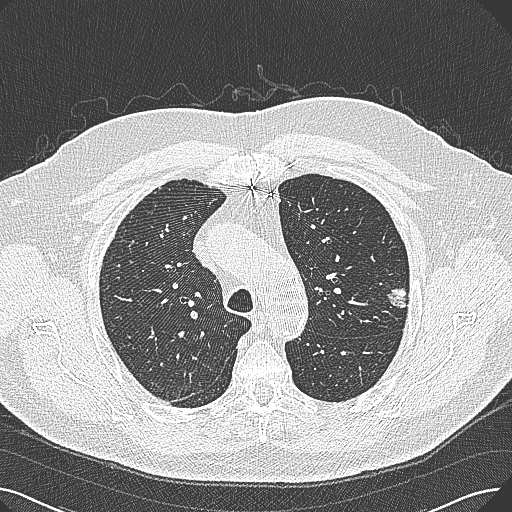
Axial slice from a low-dose chest CT screening exam, baseline screening round, lung window (W 1500 / L -600 HU), lung (sharp) reconstruction kernel (B80f). Male participant, aged 74 years at enrolment. Former smoker at enrolment.
Lesion marked by an expert reader, bounding box <376,273,423,317> (left, top, right, bottom; pixels). Screening reader's record for this exam (one nodule recorded; not confirmed to be the boxed lesion): non-calcified nodule or mass ≥4 mm, left upper lobe, 15 × 10 mm, poorly defined margins, soft tissue attenuation. Official screen result: positive, change unspecified: nodule(s) >= 4 mm or enlarging nodule(s), mass(es), or other non-specific abnormalities suspicious for lung cancer. Participant outcome: lung cancer diagnosed 124 days after this screen — adenocarcinoma, NOS, left upper lobe, well differentiated (G1), stage IA (AJCC 6th edition), 26 mm at pathology.